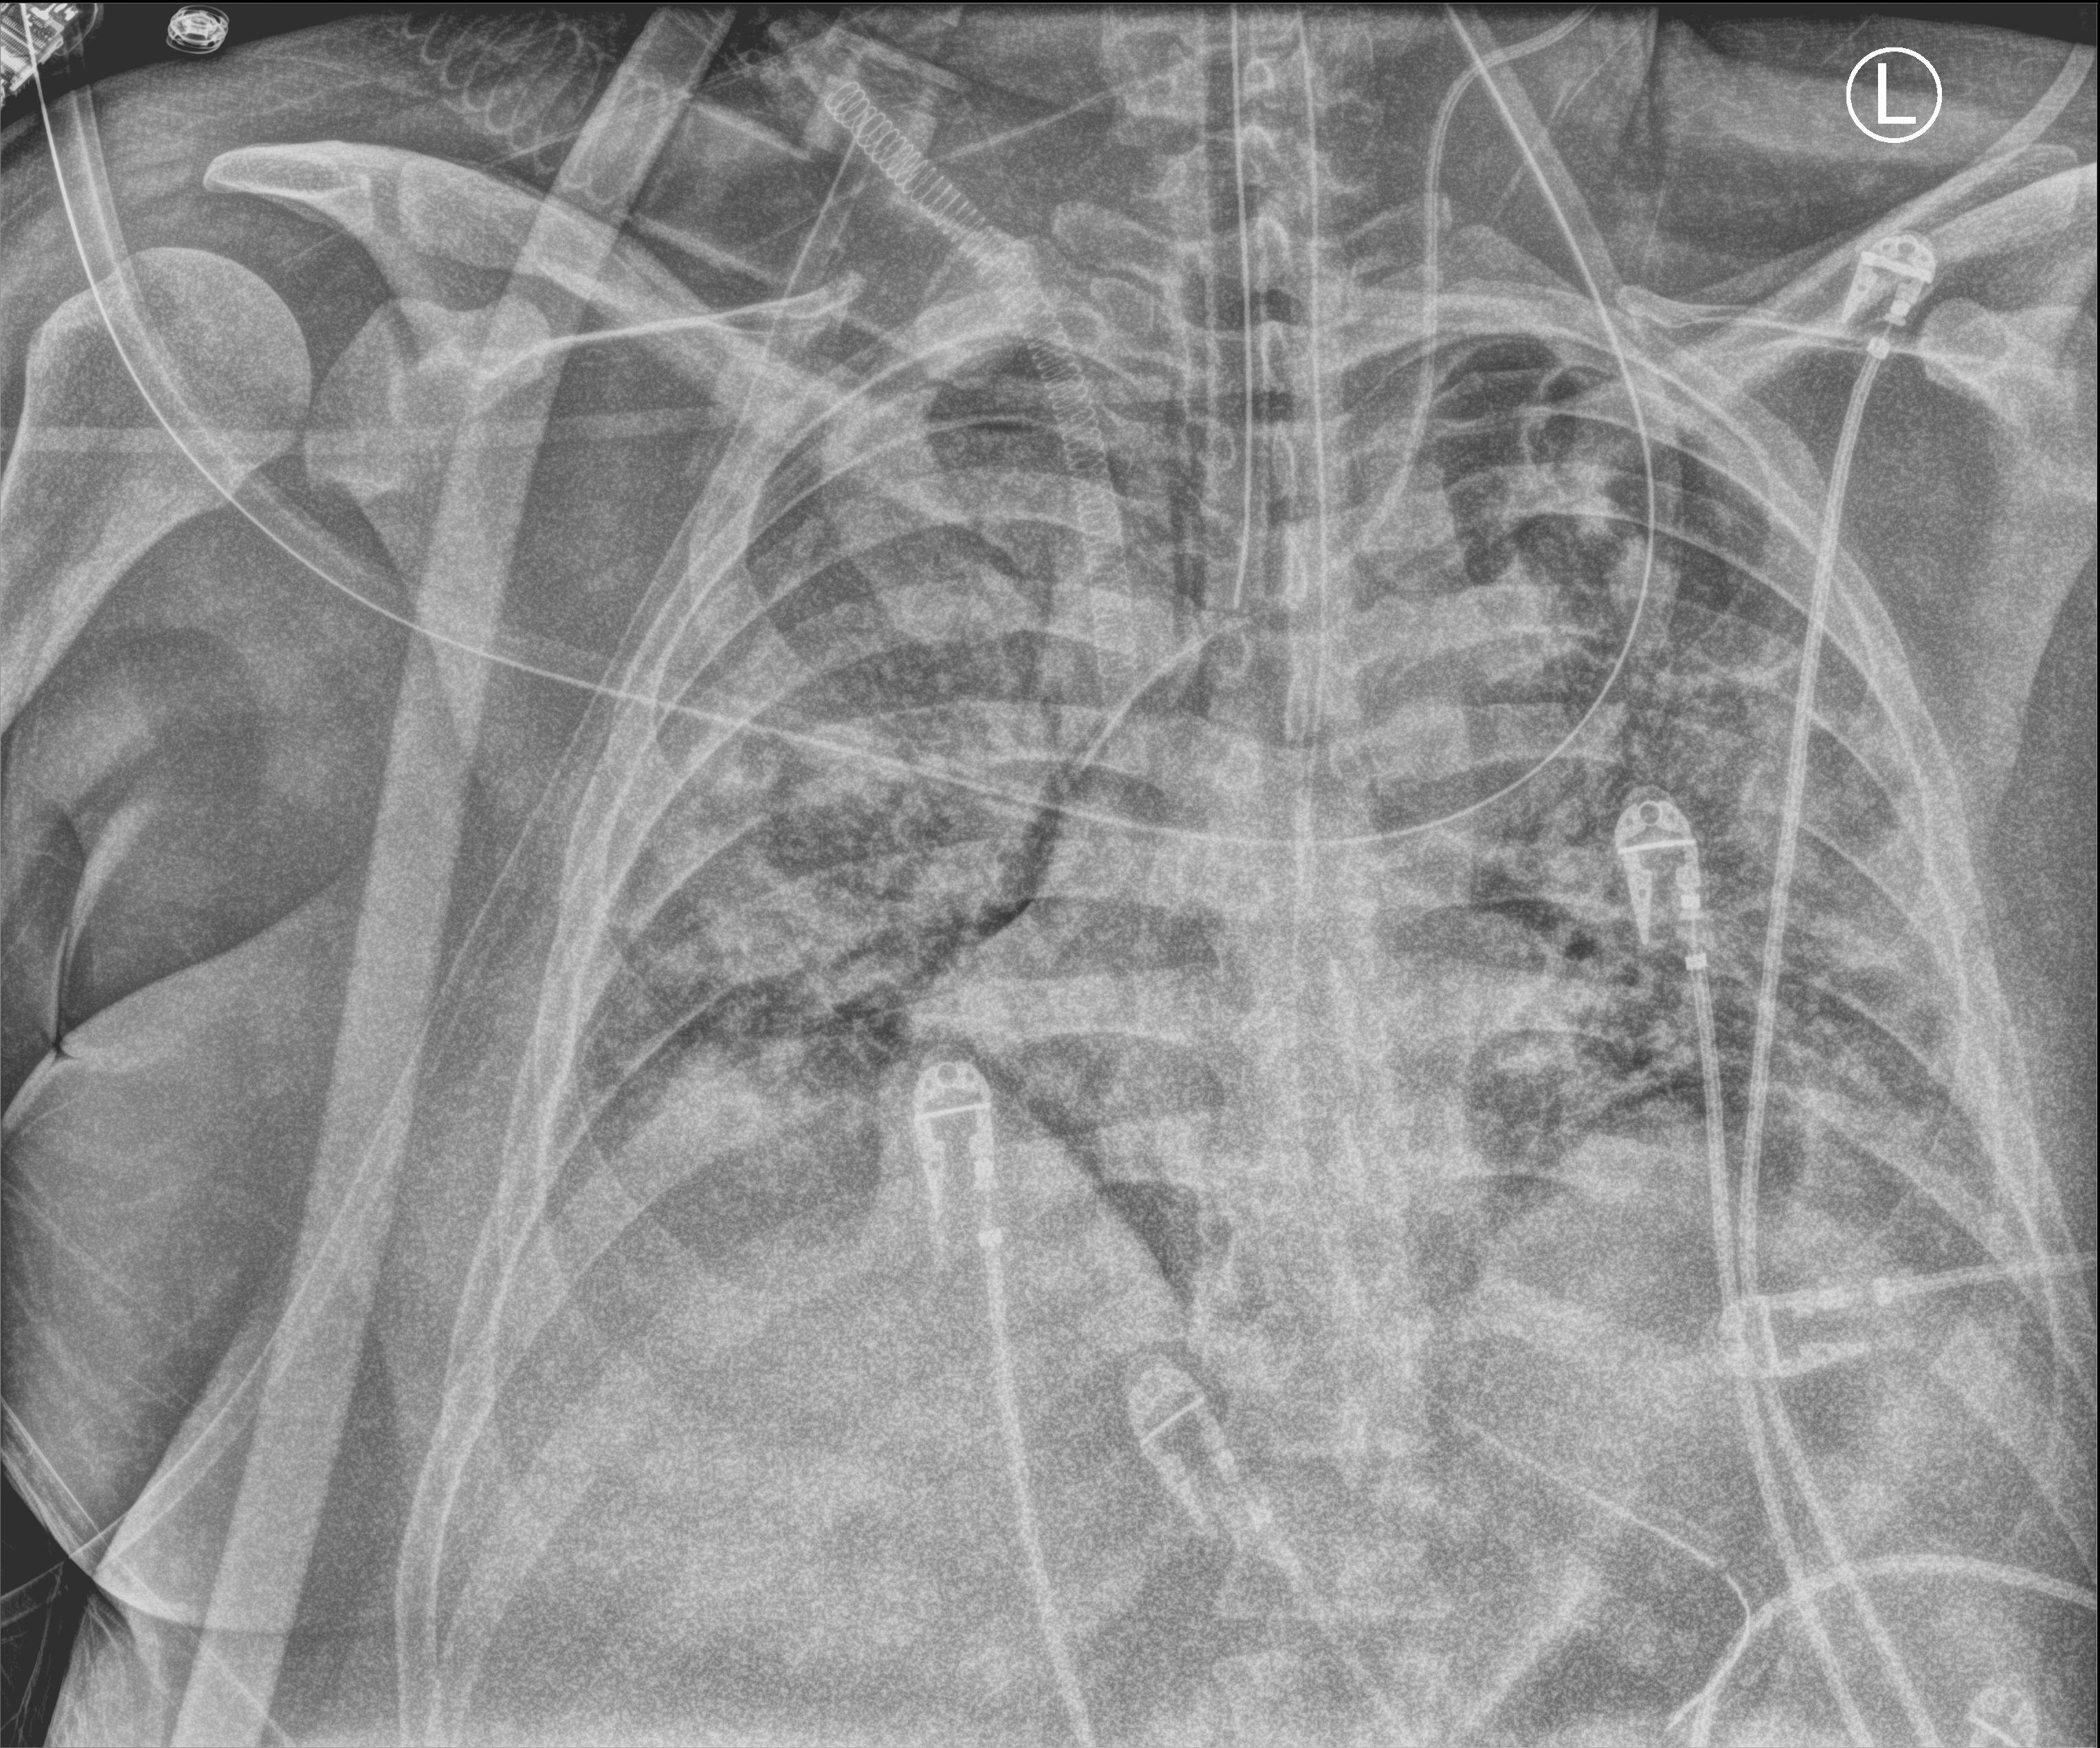
Bedside chest radiograph (computed radiography), anteroposterior (AP) projection. Patient hospitalised with COVID-19, aged 18–59 years.
Admission-level facts for this patient (not findings on this image; timing relative to this image not recorded): length of hospital stay: 15 days; admitted to intensive care during this hospital stay: yes.